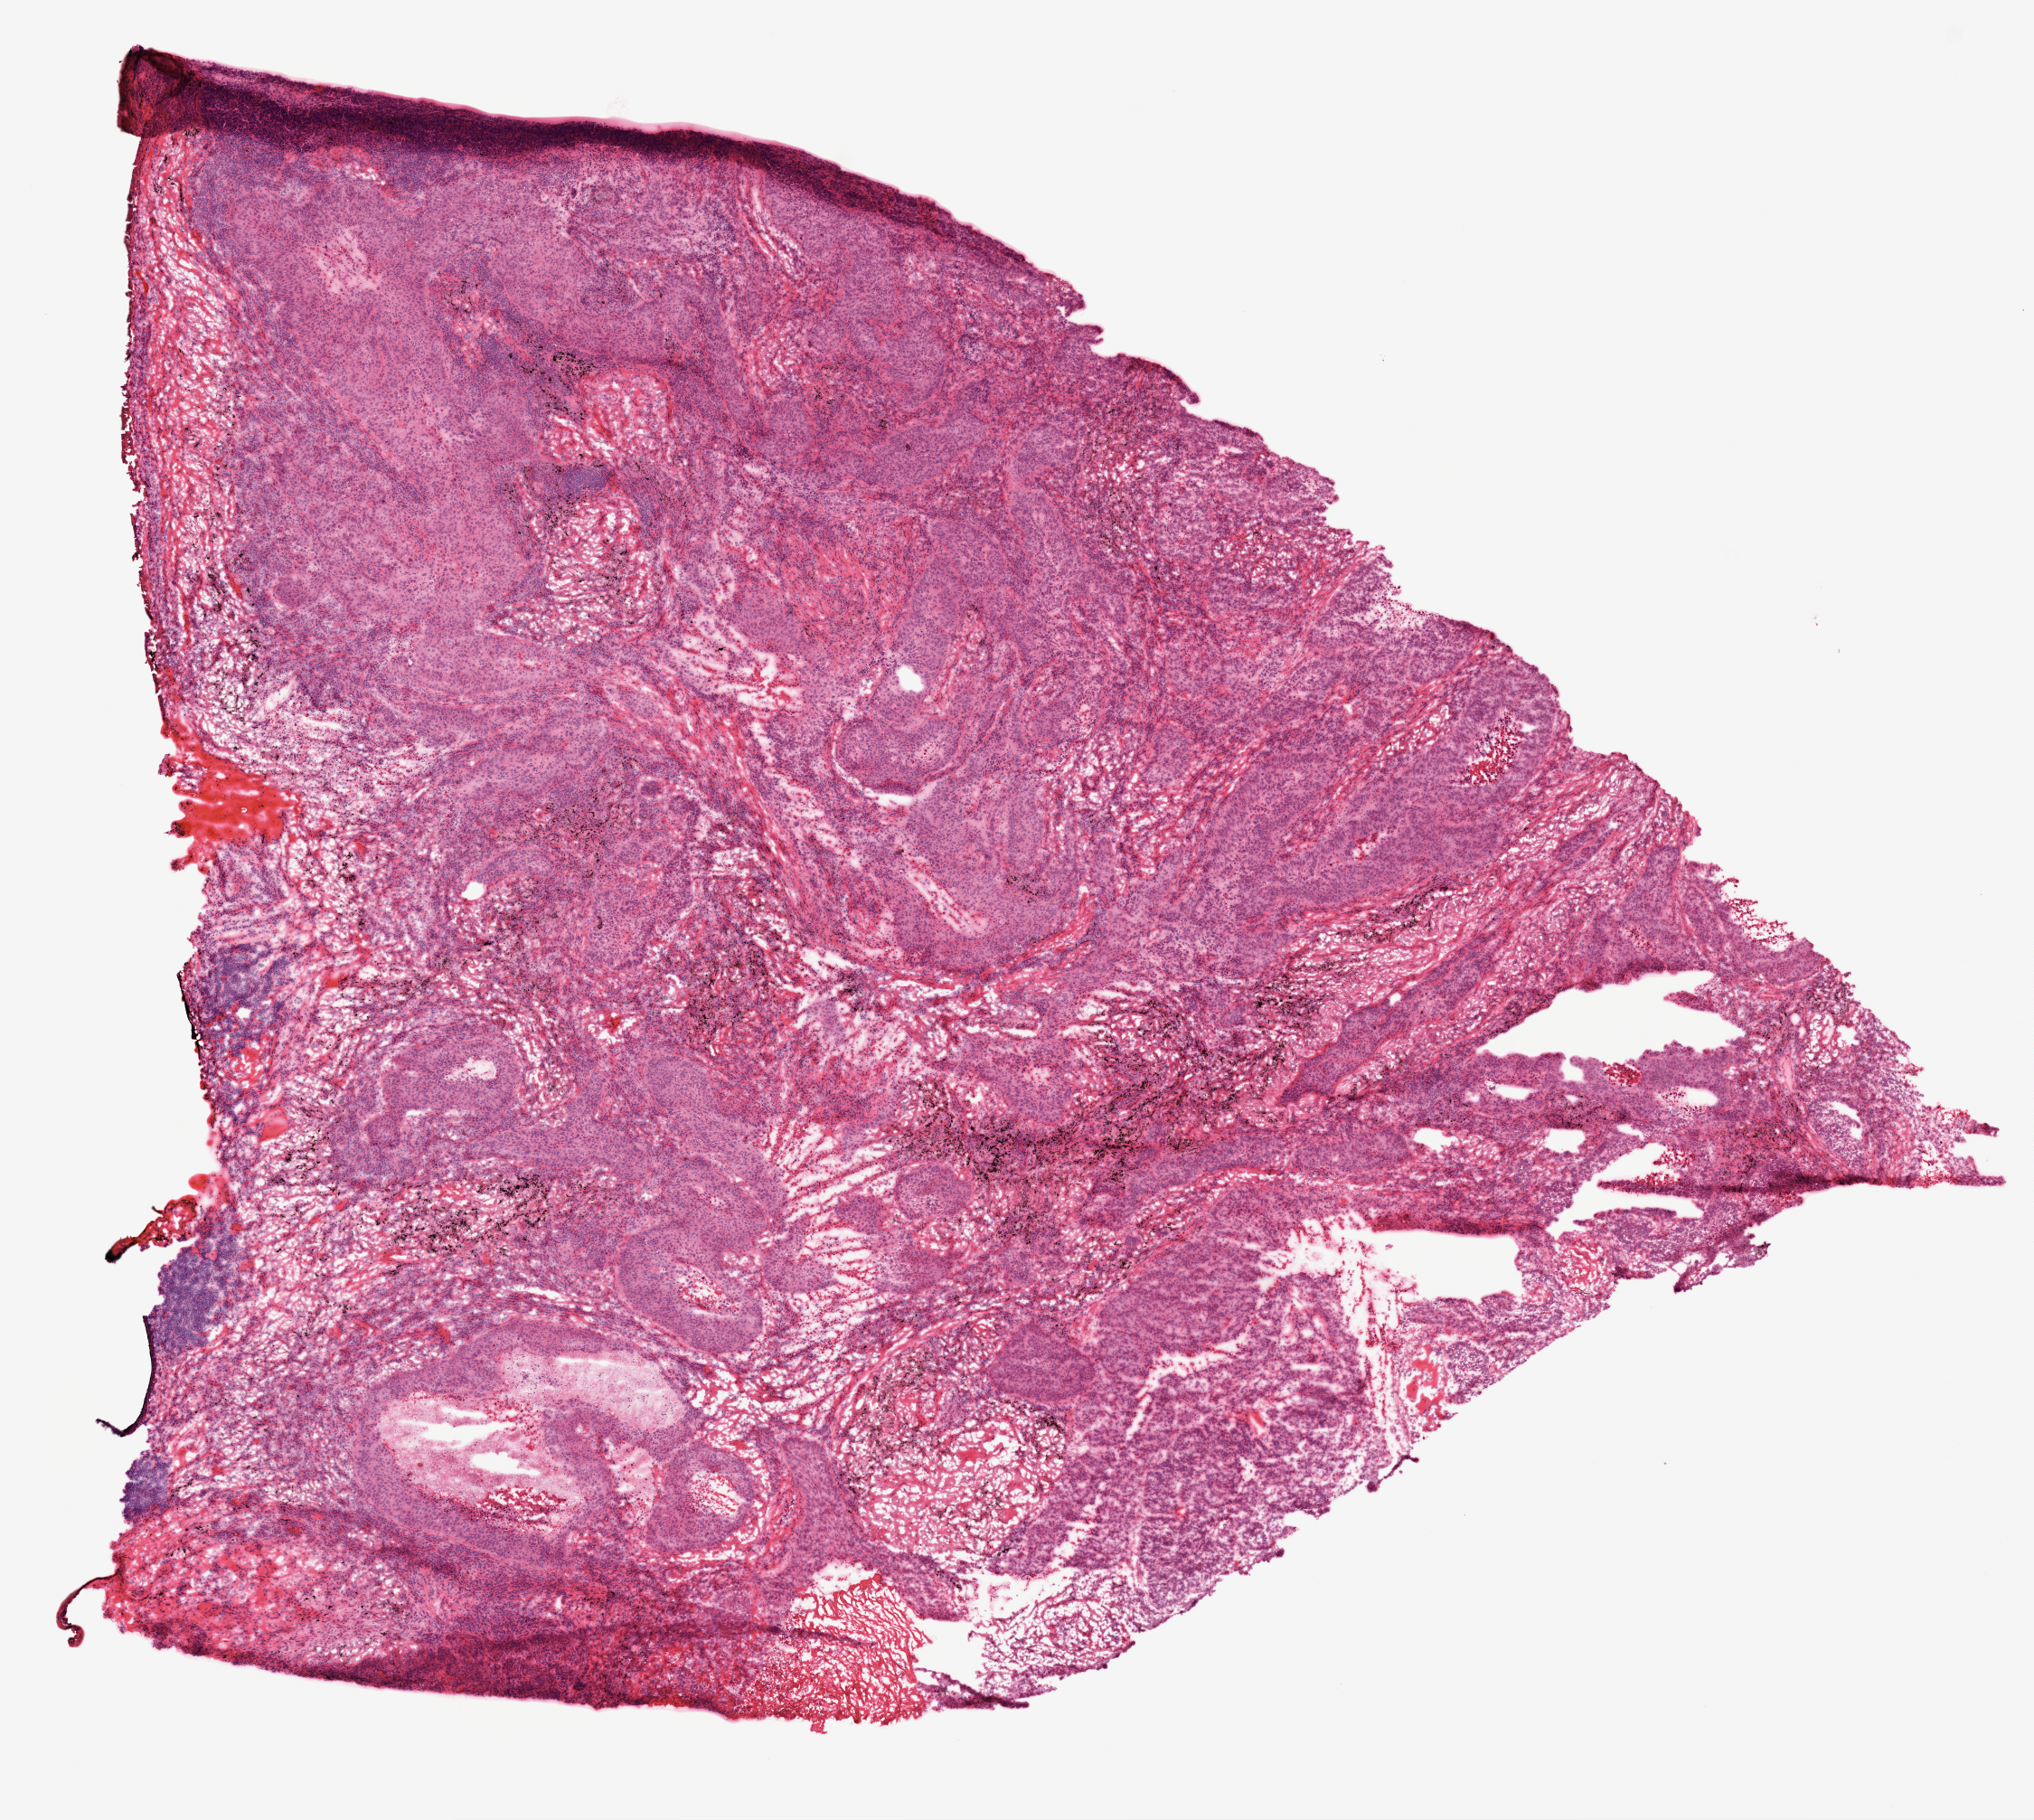
Hematoxylin and eosin (H&E) stained whole-slide image — shown as a low-resolution overview of the whole scanned area (about 9.0 x 8.1 mm, acquisition: 20x scan); frozen section from the top of the tissue portion; primary tumour sample from the lung. Male, age 74 years at initial diagnosis. Composition of this section per pathologist review: tumour cells 92%, tumour nuclei 71%, normal cells 0%, stromal cells 0%, necrosis 8%. Infiltration values recorded for this section: lymphocyte infiltration 20%, monocyte infiltration 1%, neutrophil infiltration 1%.
Laterality: left. TNM: T2a N0 M0. Pathologic diagnosis: Squamous cell carcinoma, NOS (upper lobe, lung). AJCC pathologic stage: IB.